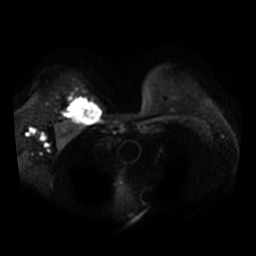
Breast MRI, one axial slice. Slice 26 of 36 in the series (ordered by position). Diffusion-weighted series; image 2 of 4 stored at this slice position (different b-values; order by instance number). 3 T. 5 mm slice thickness. 256 × 256 image matrix, field of view 340 × 340 mm. Female patient.
Outlined on this slice (outlined manually by an expert reader):
- tumour on diffusion-weighted imaging: bounding box (x1, y1, x2, y2) in pixels: (68, 99, 100, 124)